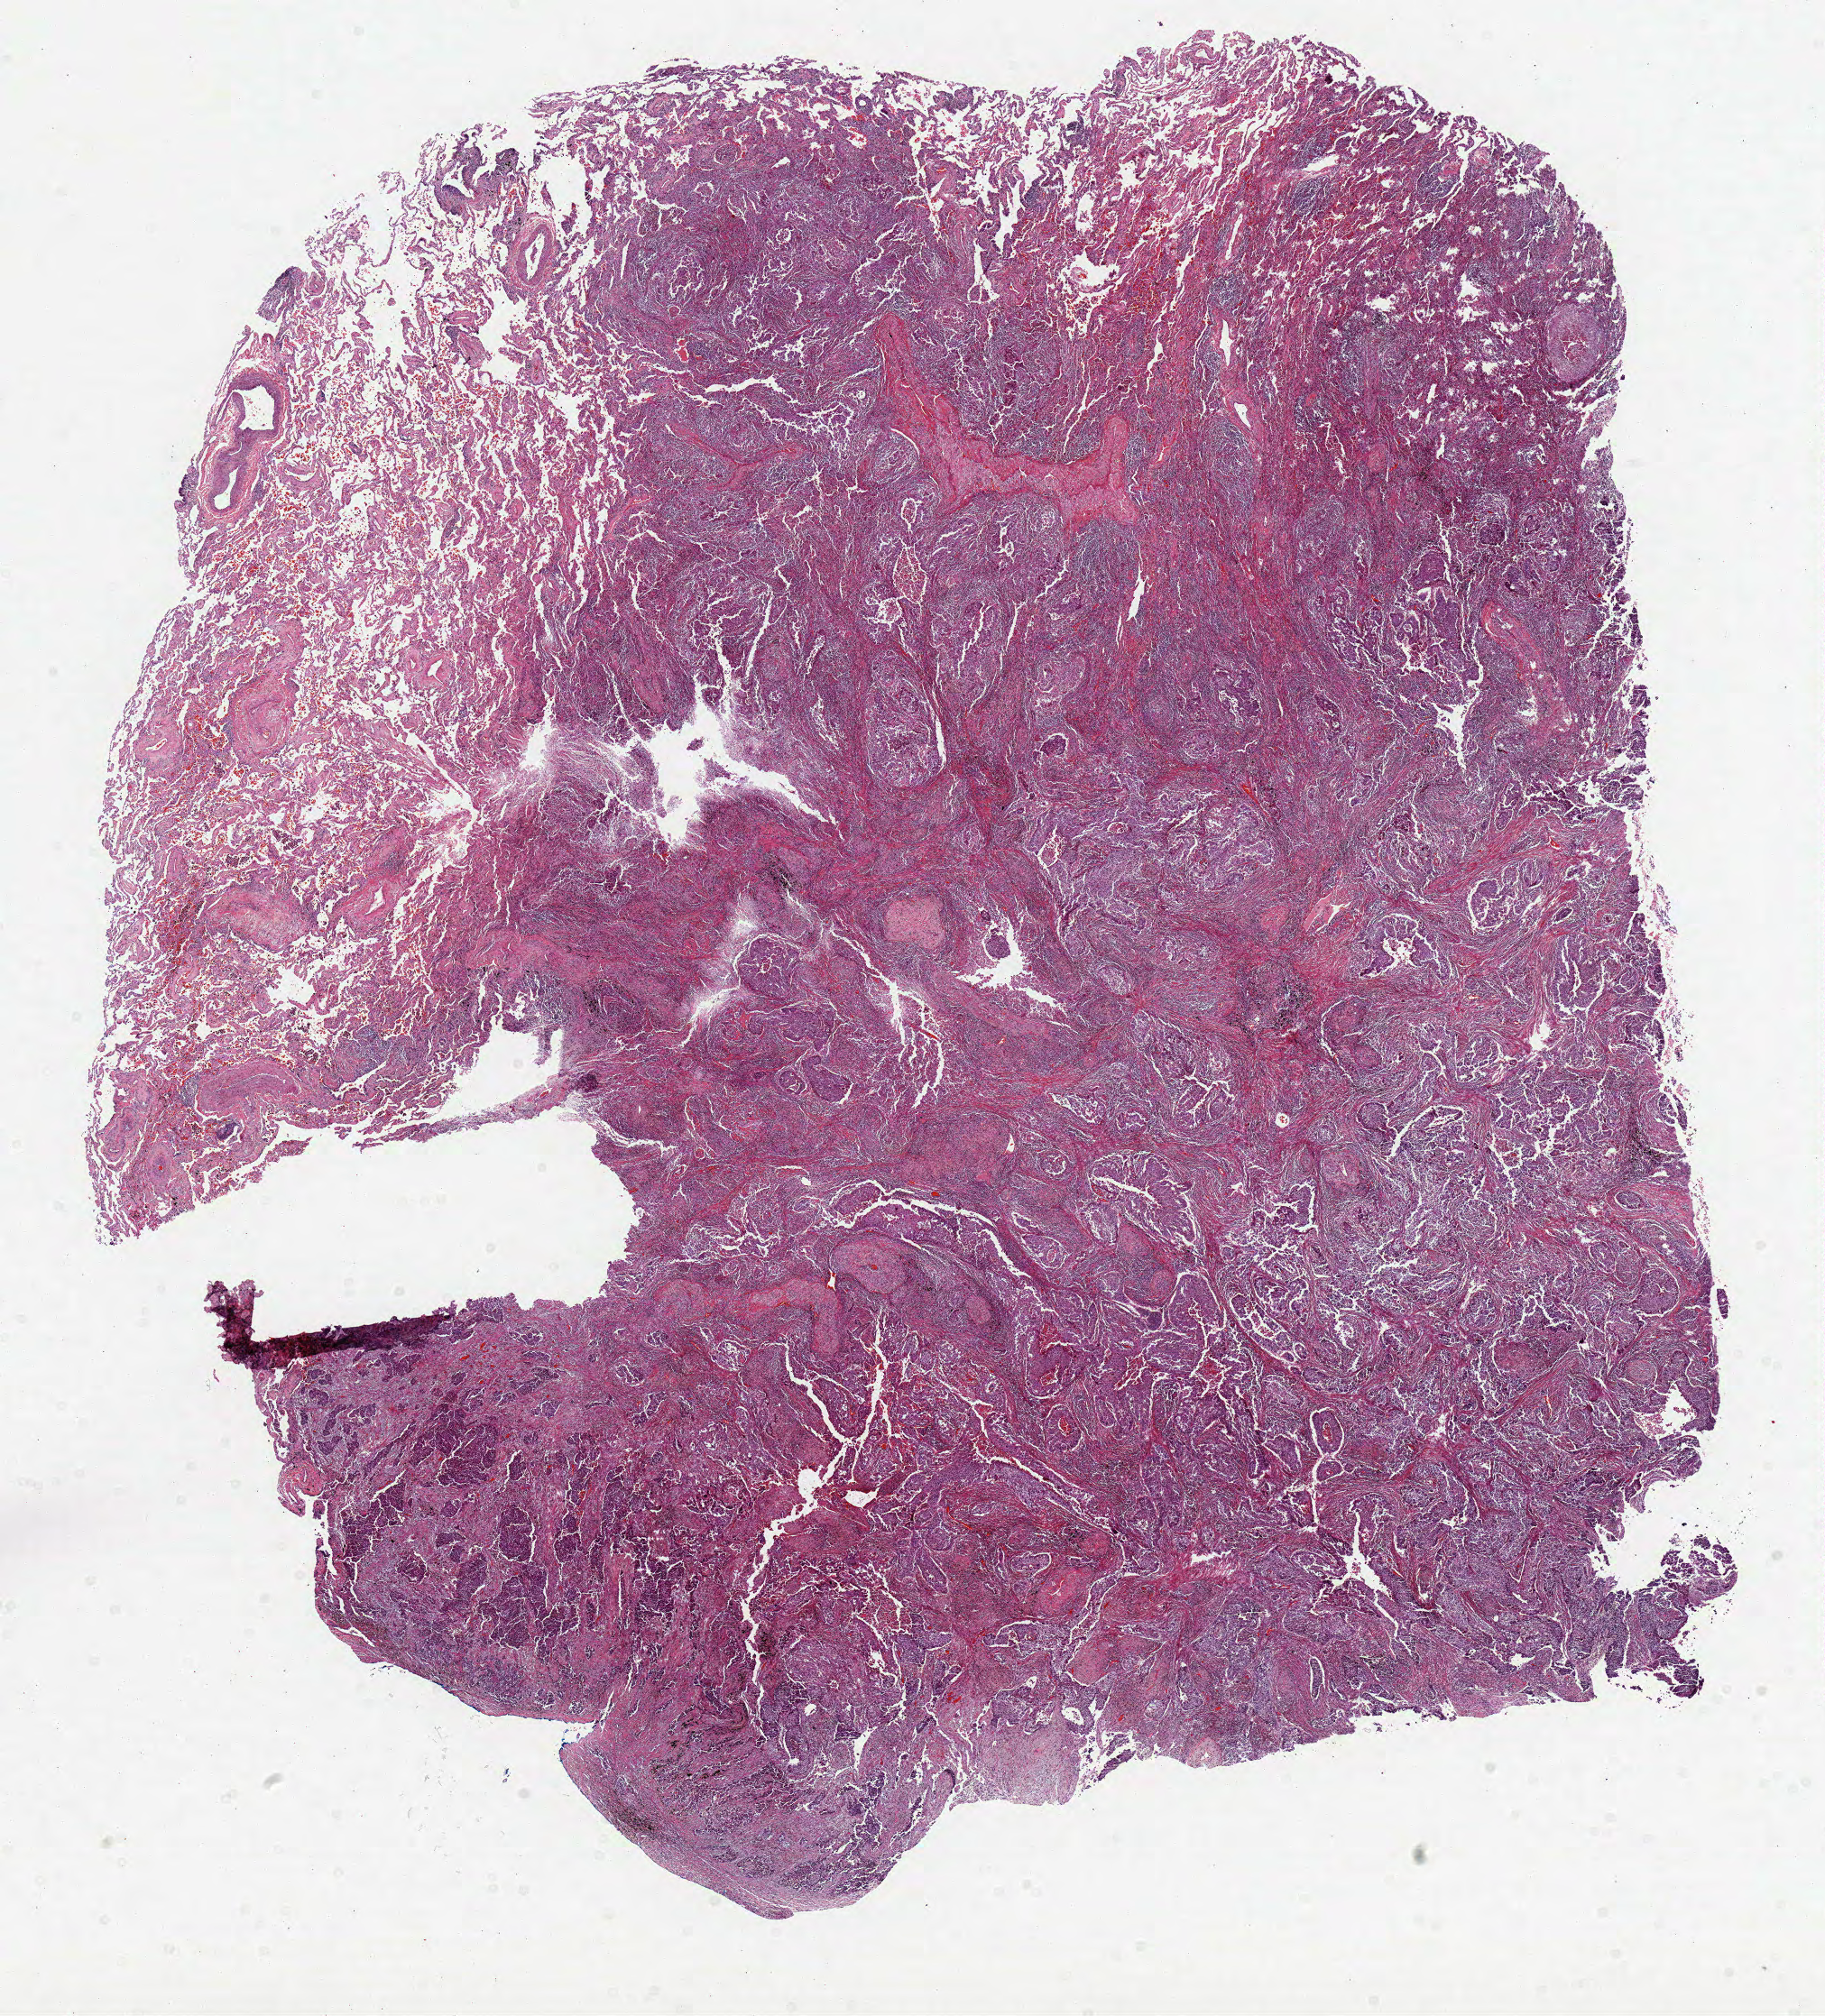
H&E whole-slide image — low-resolution overview of the scanned area, about 16.3 x 18.0 mm (acquisition: 20x scan), formalin-fixed paraffin-embedded (FFPE) diagnostic section, primary tumour sample from the lung. Patient: male, age at initial diagnosis 70 years.
* histologic diagnosis: Squamous cell carcinoma, NOS (upper lobe, lung)
* AJCC pathologic stage: IB